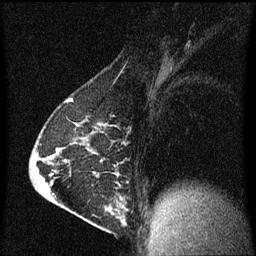
Breast MRI (dynamic contrast-enhanced), one sagittal slice. Position 38 of 60 along the scan axis. Dynamic contrast-enhanced series, image 2 of 3 at this slice position (ordered by acquisition). 1.5 T. TE 4.2 ms, TR 8 ms. 256 × 256 image matrix, field of view 200 × 200 mm. Patient: female, 63 years.
Outlined on this slice (semi-automatically segmented with operator editing):
- analysis volume of interest (the breast-tissue region the enhancement analysis was run in; not a lesion): bounding box (x1, y1, x2, y2) in pixels: (88, 182, 129, 229)
- tumour enhancement mask (voxels above the 70 % enhancement threshold inside the analysis volume of interest): (112, 214, 125, 223)